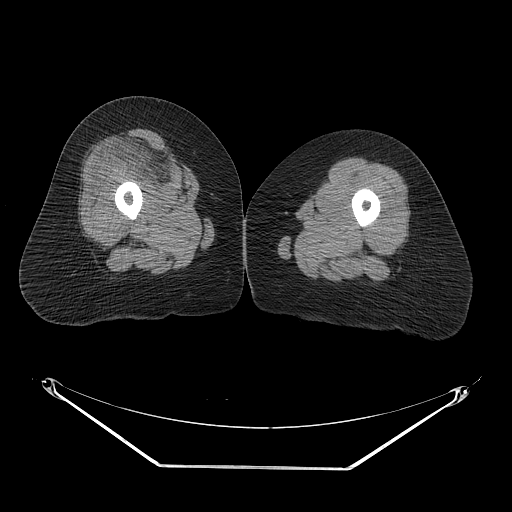
CT of an extremity soft-tissue mass (from a PET/CT study), one axial slice. Position 24 of 267 along the scan axis. Reconstruction kernel STANDARD. 140 kVp. Soft-tissue window (W 400 / L 40 HU). 3.75 mm slice thickness. 512 × 512 image matrix, field of view 500 × 500 mm. Female patient. From the clinical record (not read from this slice): histological type: malignant solitary fibrous tumor; grade: intermediate; site of the primary tumour: right thigh.
Structures marked on this image (expert contour drawn on MRI and transferred to this co-registered scan by the dataset authors):
- gross tumour volume including surrounding oedema: bounding box [x1, y1, x2, y2] px = [107, 130, 200, 200]
- gross tumour volume (mass): [116, 144, 177, 188]